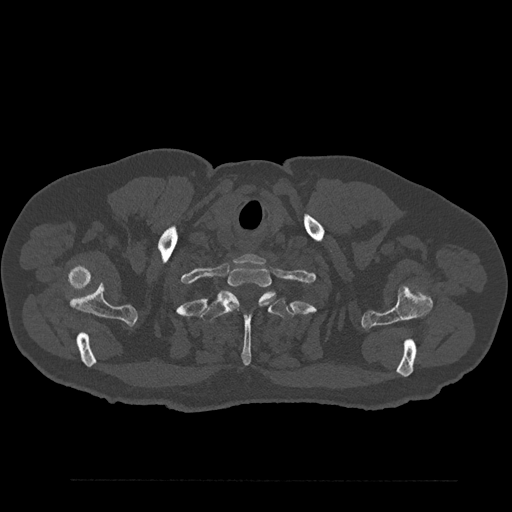
CT including the spine, one axial slice; position 737 of 797 along the scan axis; 120 kVp; bone window (W 1800 / L 400 HU); 0.5 mm slice thickness; 512 × 512 image matrix. Male patient, age 61 years. Case-level facts recorded for this patient, not image findings: primary cancer: prostate.
Outlined on this slice (semi-automatically segmented with operator editing):
- T1 vertebra: bounding box (x1, y1, x2, y2) in pixels: (219, 267, 271, 305)
- T2 vertebra: (201, 291, 294, 366)